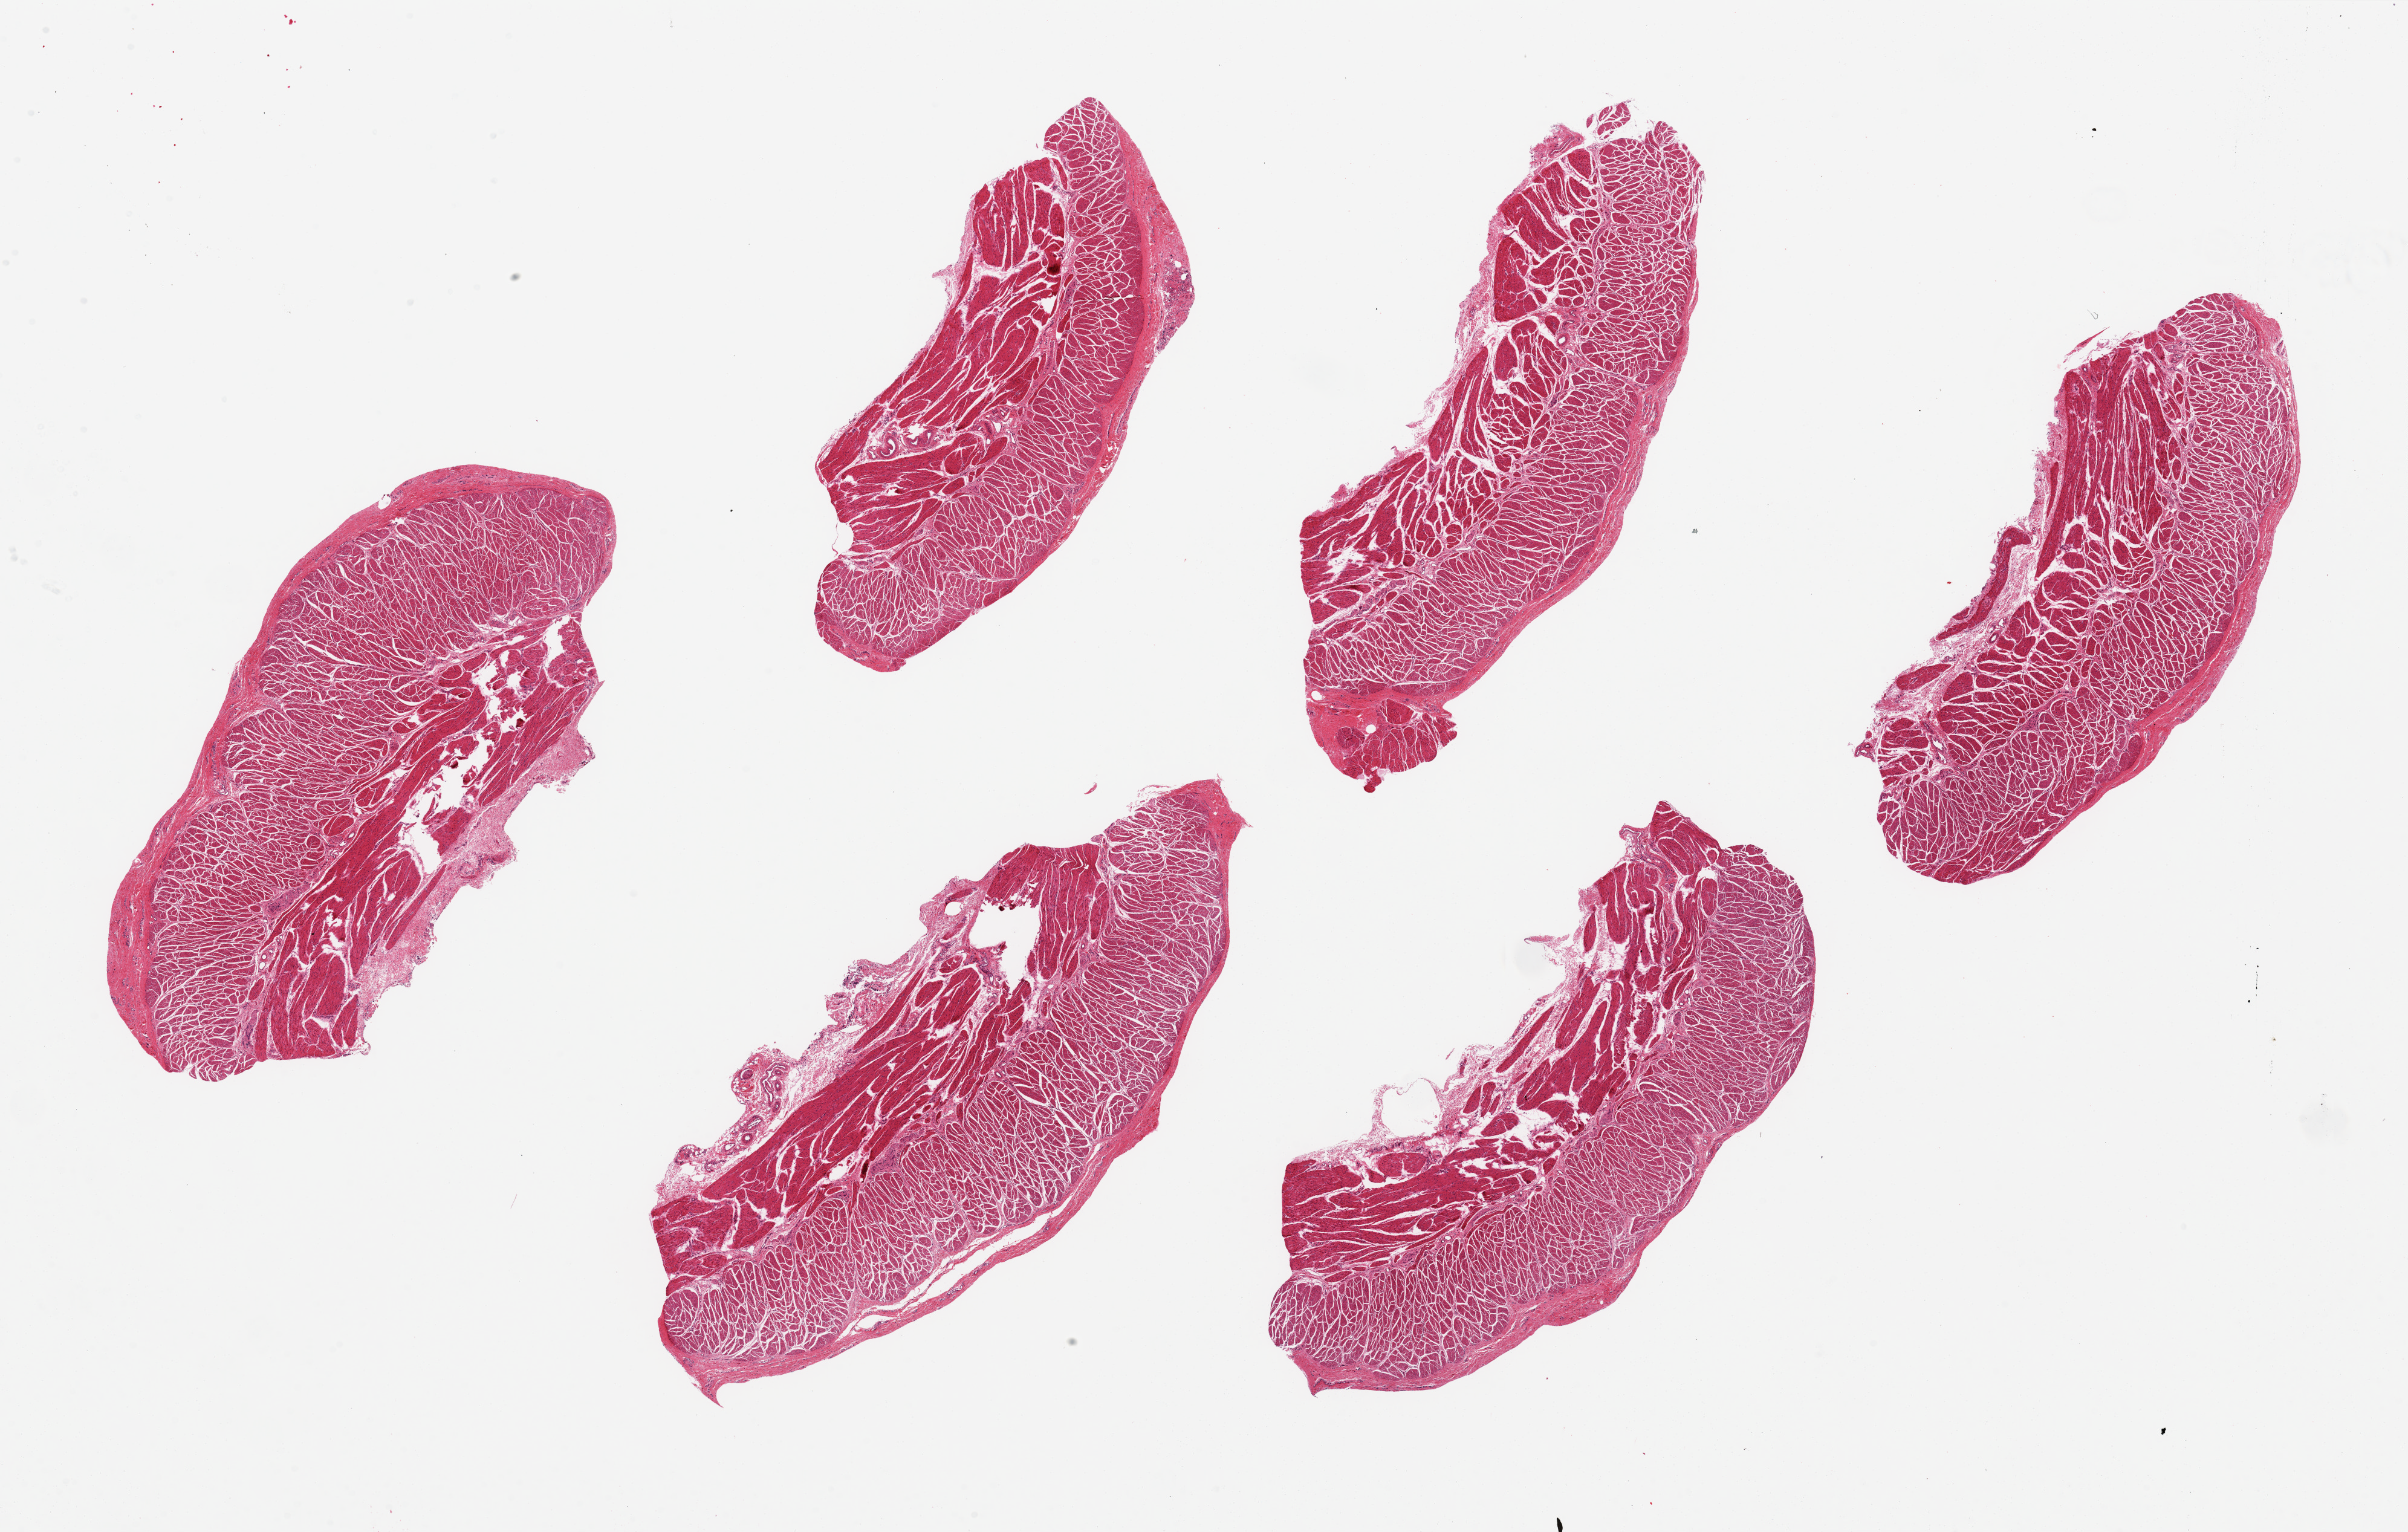
Whole-slide image, haematoxylin and eosin stain — a low-resolution overview of the entire scanned area, about 31.5 x 20.0 mm (from a 20x scan), PAXgene-fixed paraffin-embedded (PFPE) section, section of esophageal muscle (target tissue), donor tissue sample. Donor: male.
Review note (as recorded): 6 pieces, ~9x3mm.